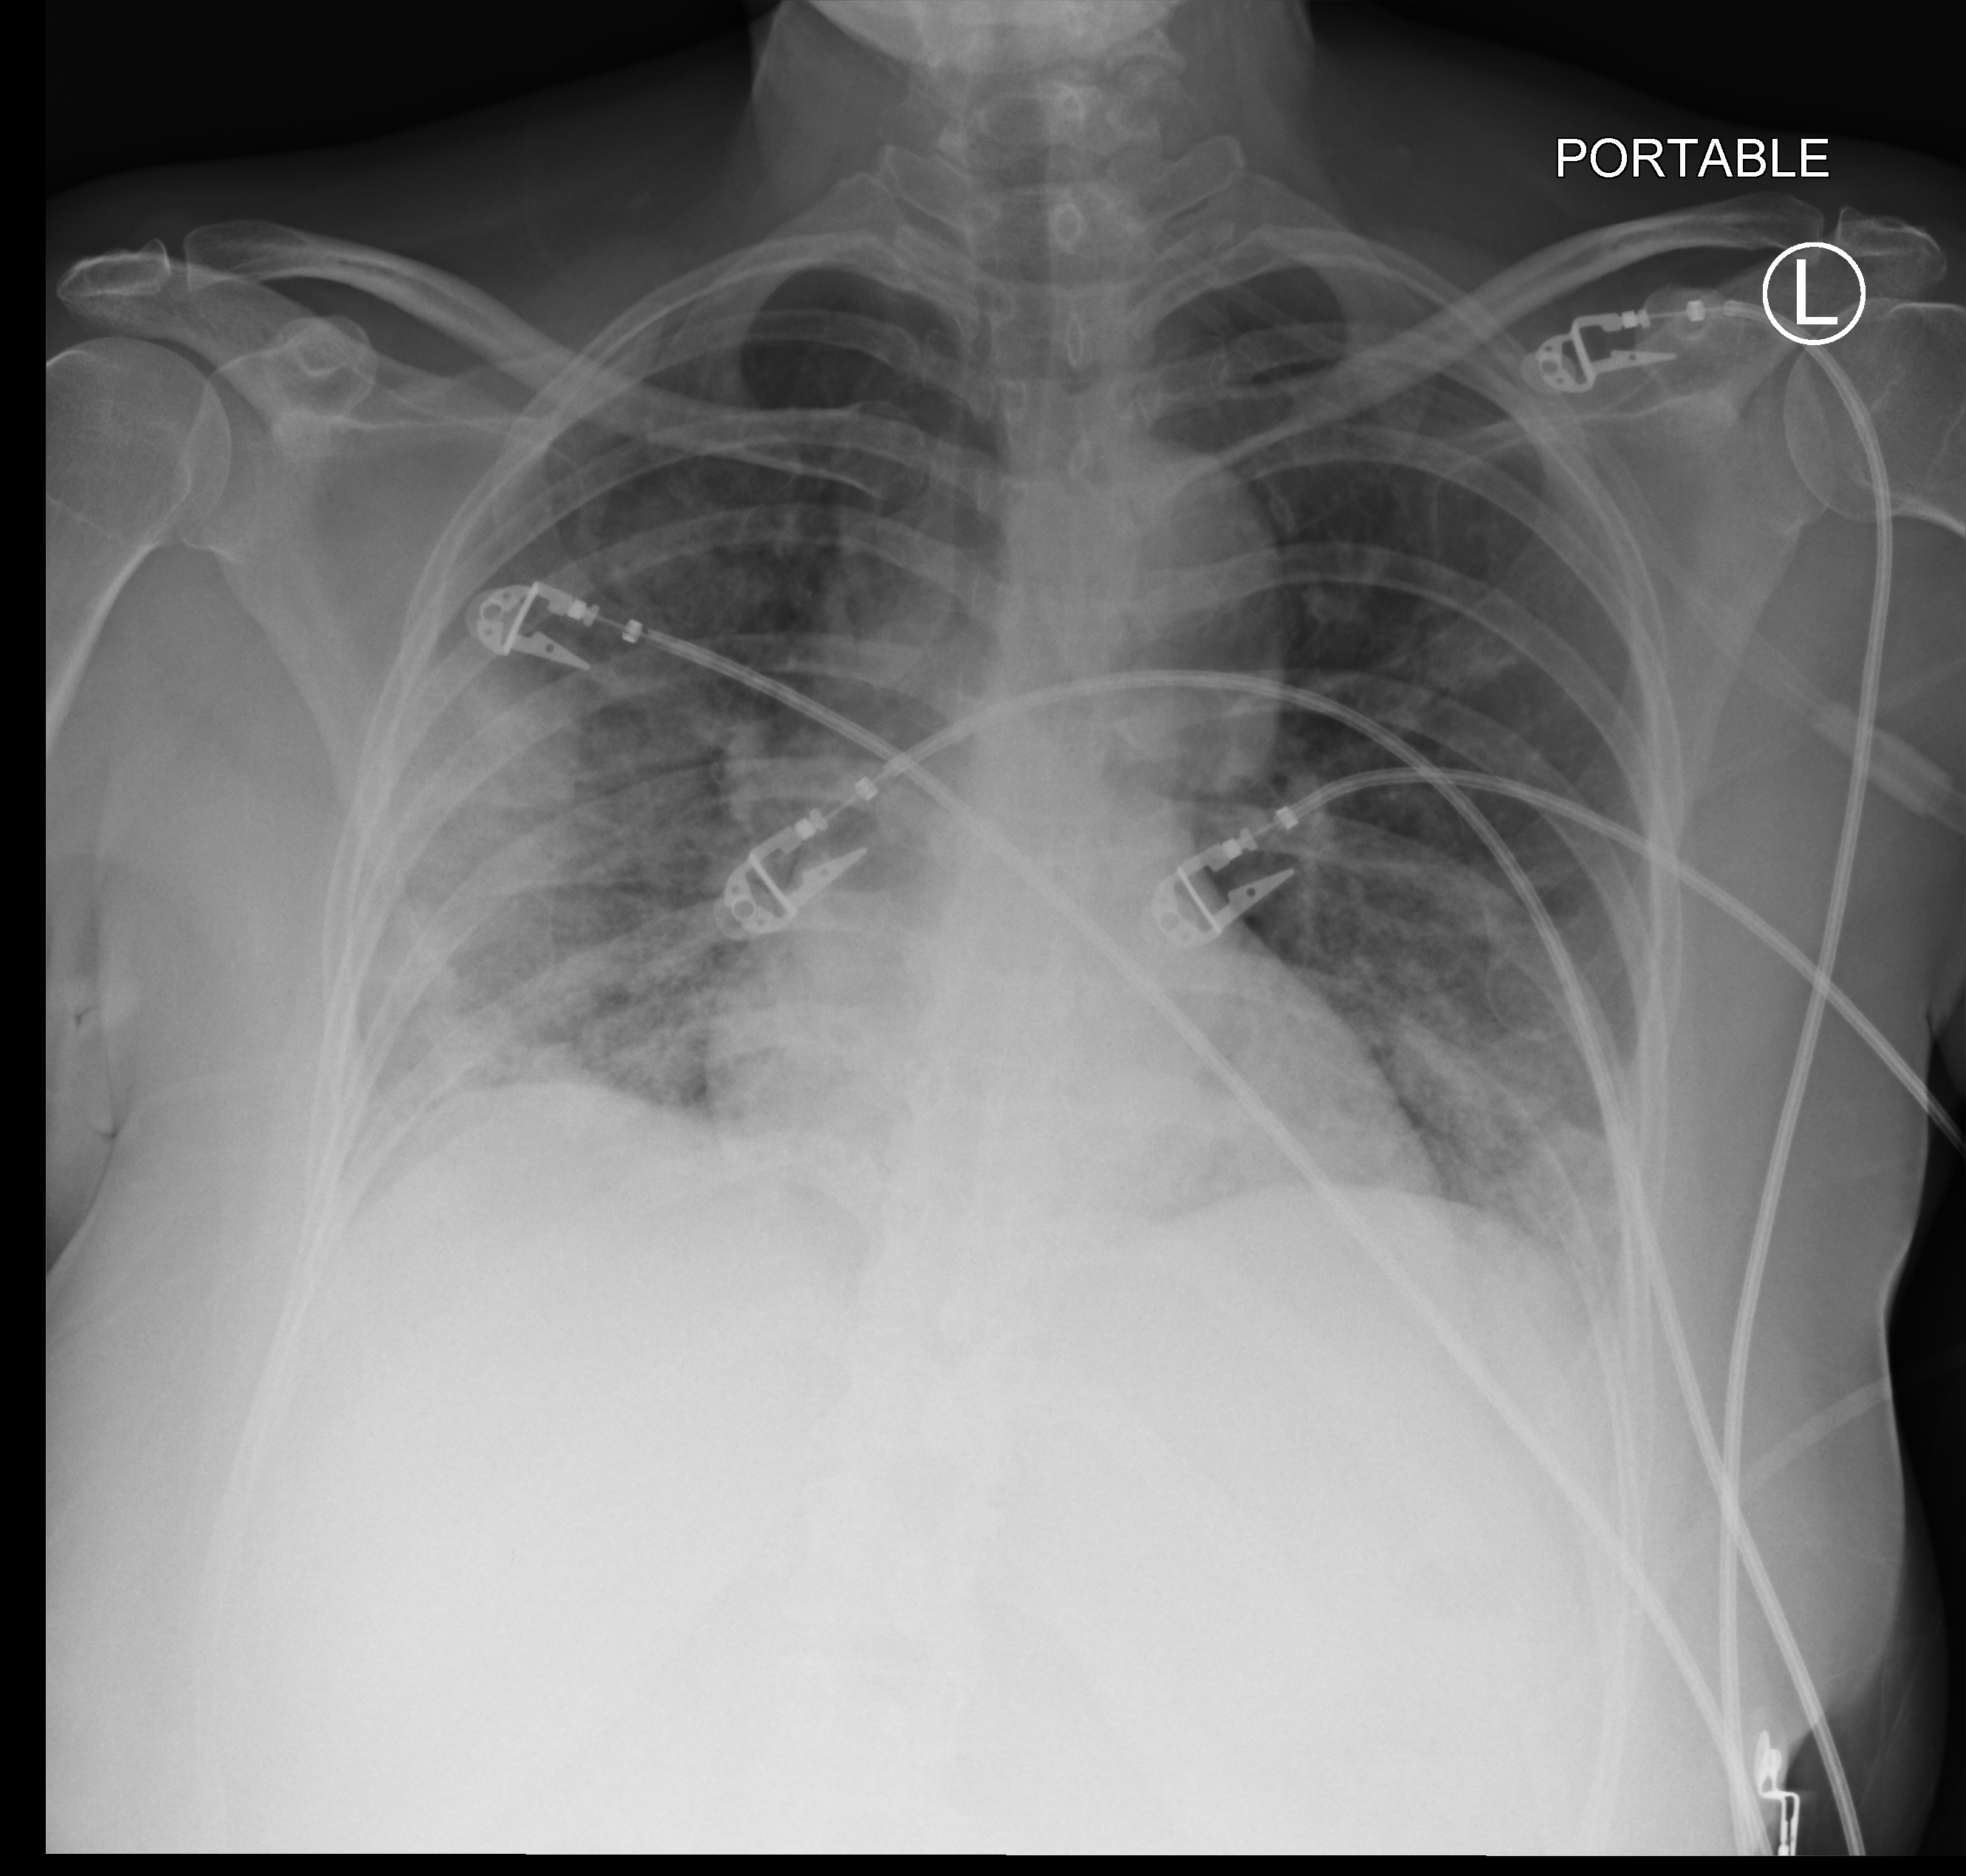
Chest X-ray (portable). Female patient hospitalised with COVID-19, age 18–59 years.
Admission-level facts for this patient (not findings on this image; timing relative to this image not recorded): mechanically ventilated during this hospital stay: yes.